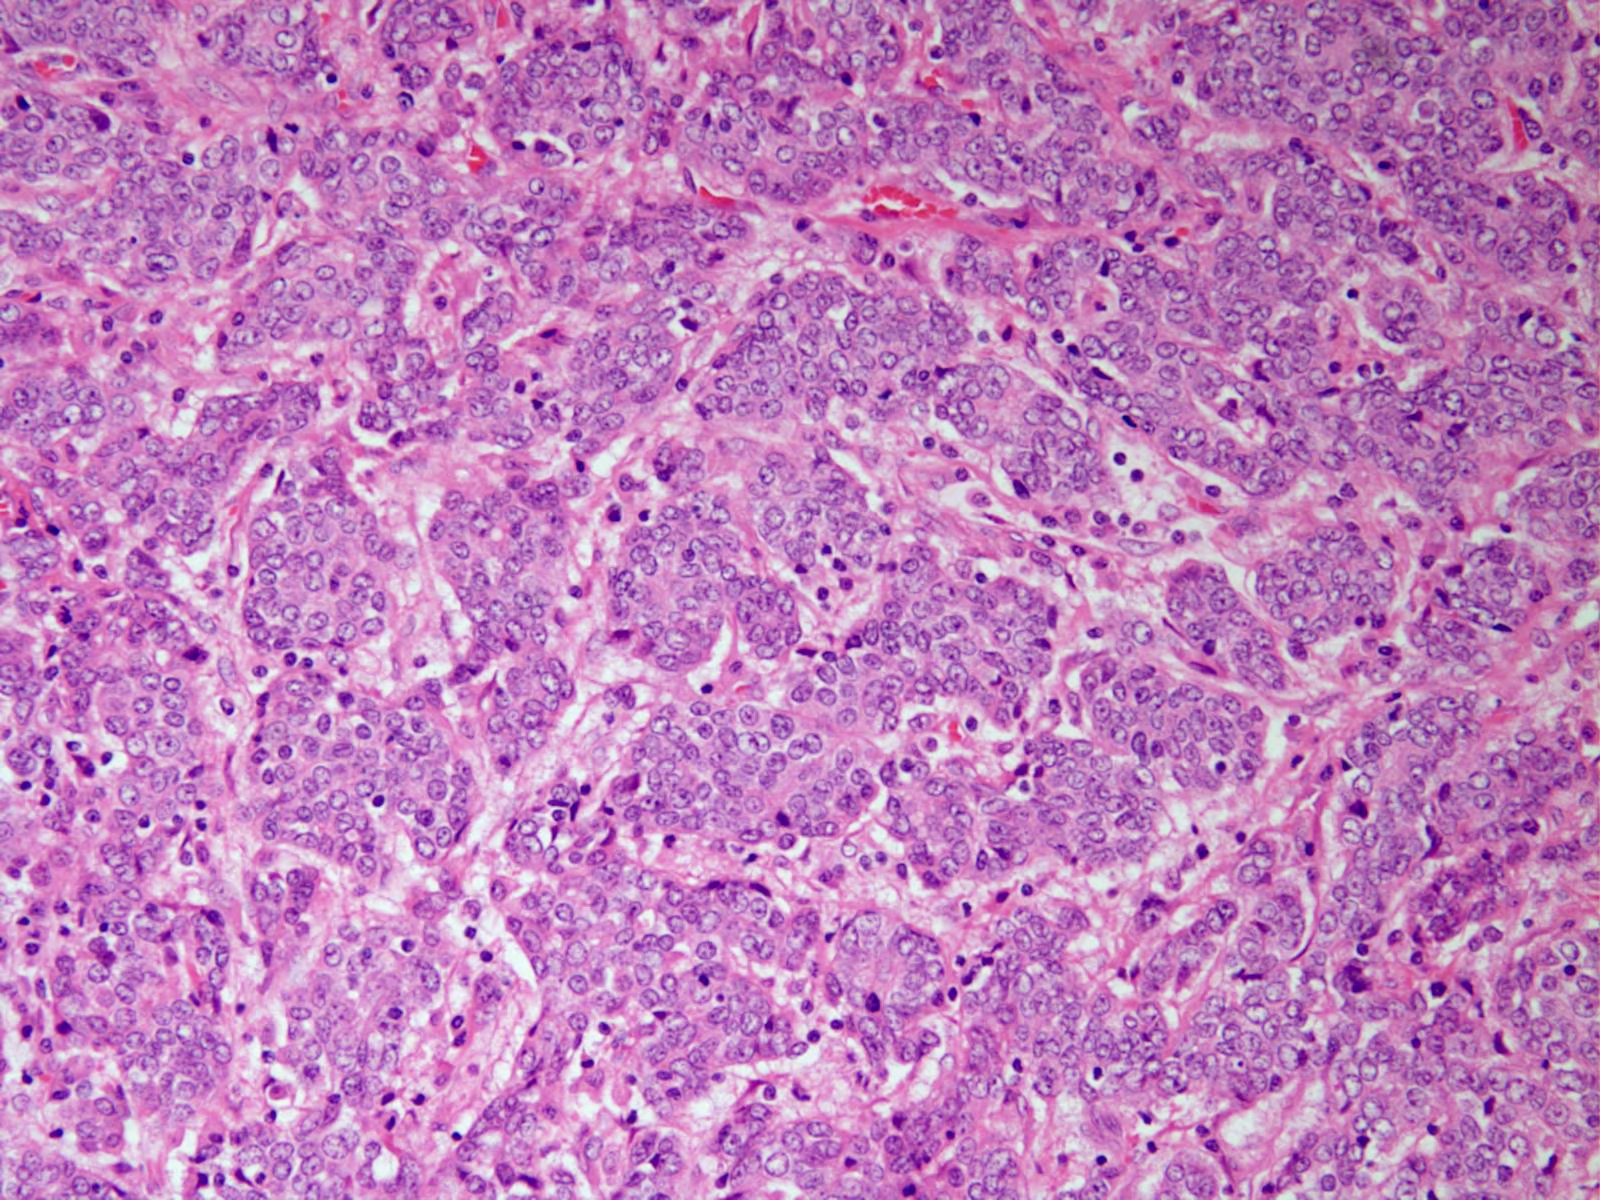
Hematoxylin and eosin (H&E) stained image of one small field of the section — roughly 0.8 x 0.6 mm in extent. Formalin-fixed paraffin-embedded (FFPE) diagnostic section. Sample: primary tumour, stomach. Patient: female, age at initial diagnosis 66 years. Histologic grade: G3 (poorly differentiated).
• AJCC pathologic stage: IIIA (6th edition)
• diagnosis: Adenocarcinoma, NOS
• lymph nodes positive (case pathology): 0 of 8 examined